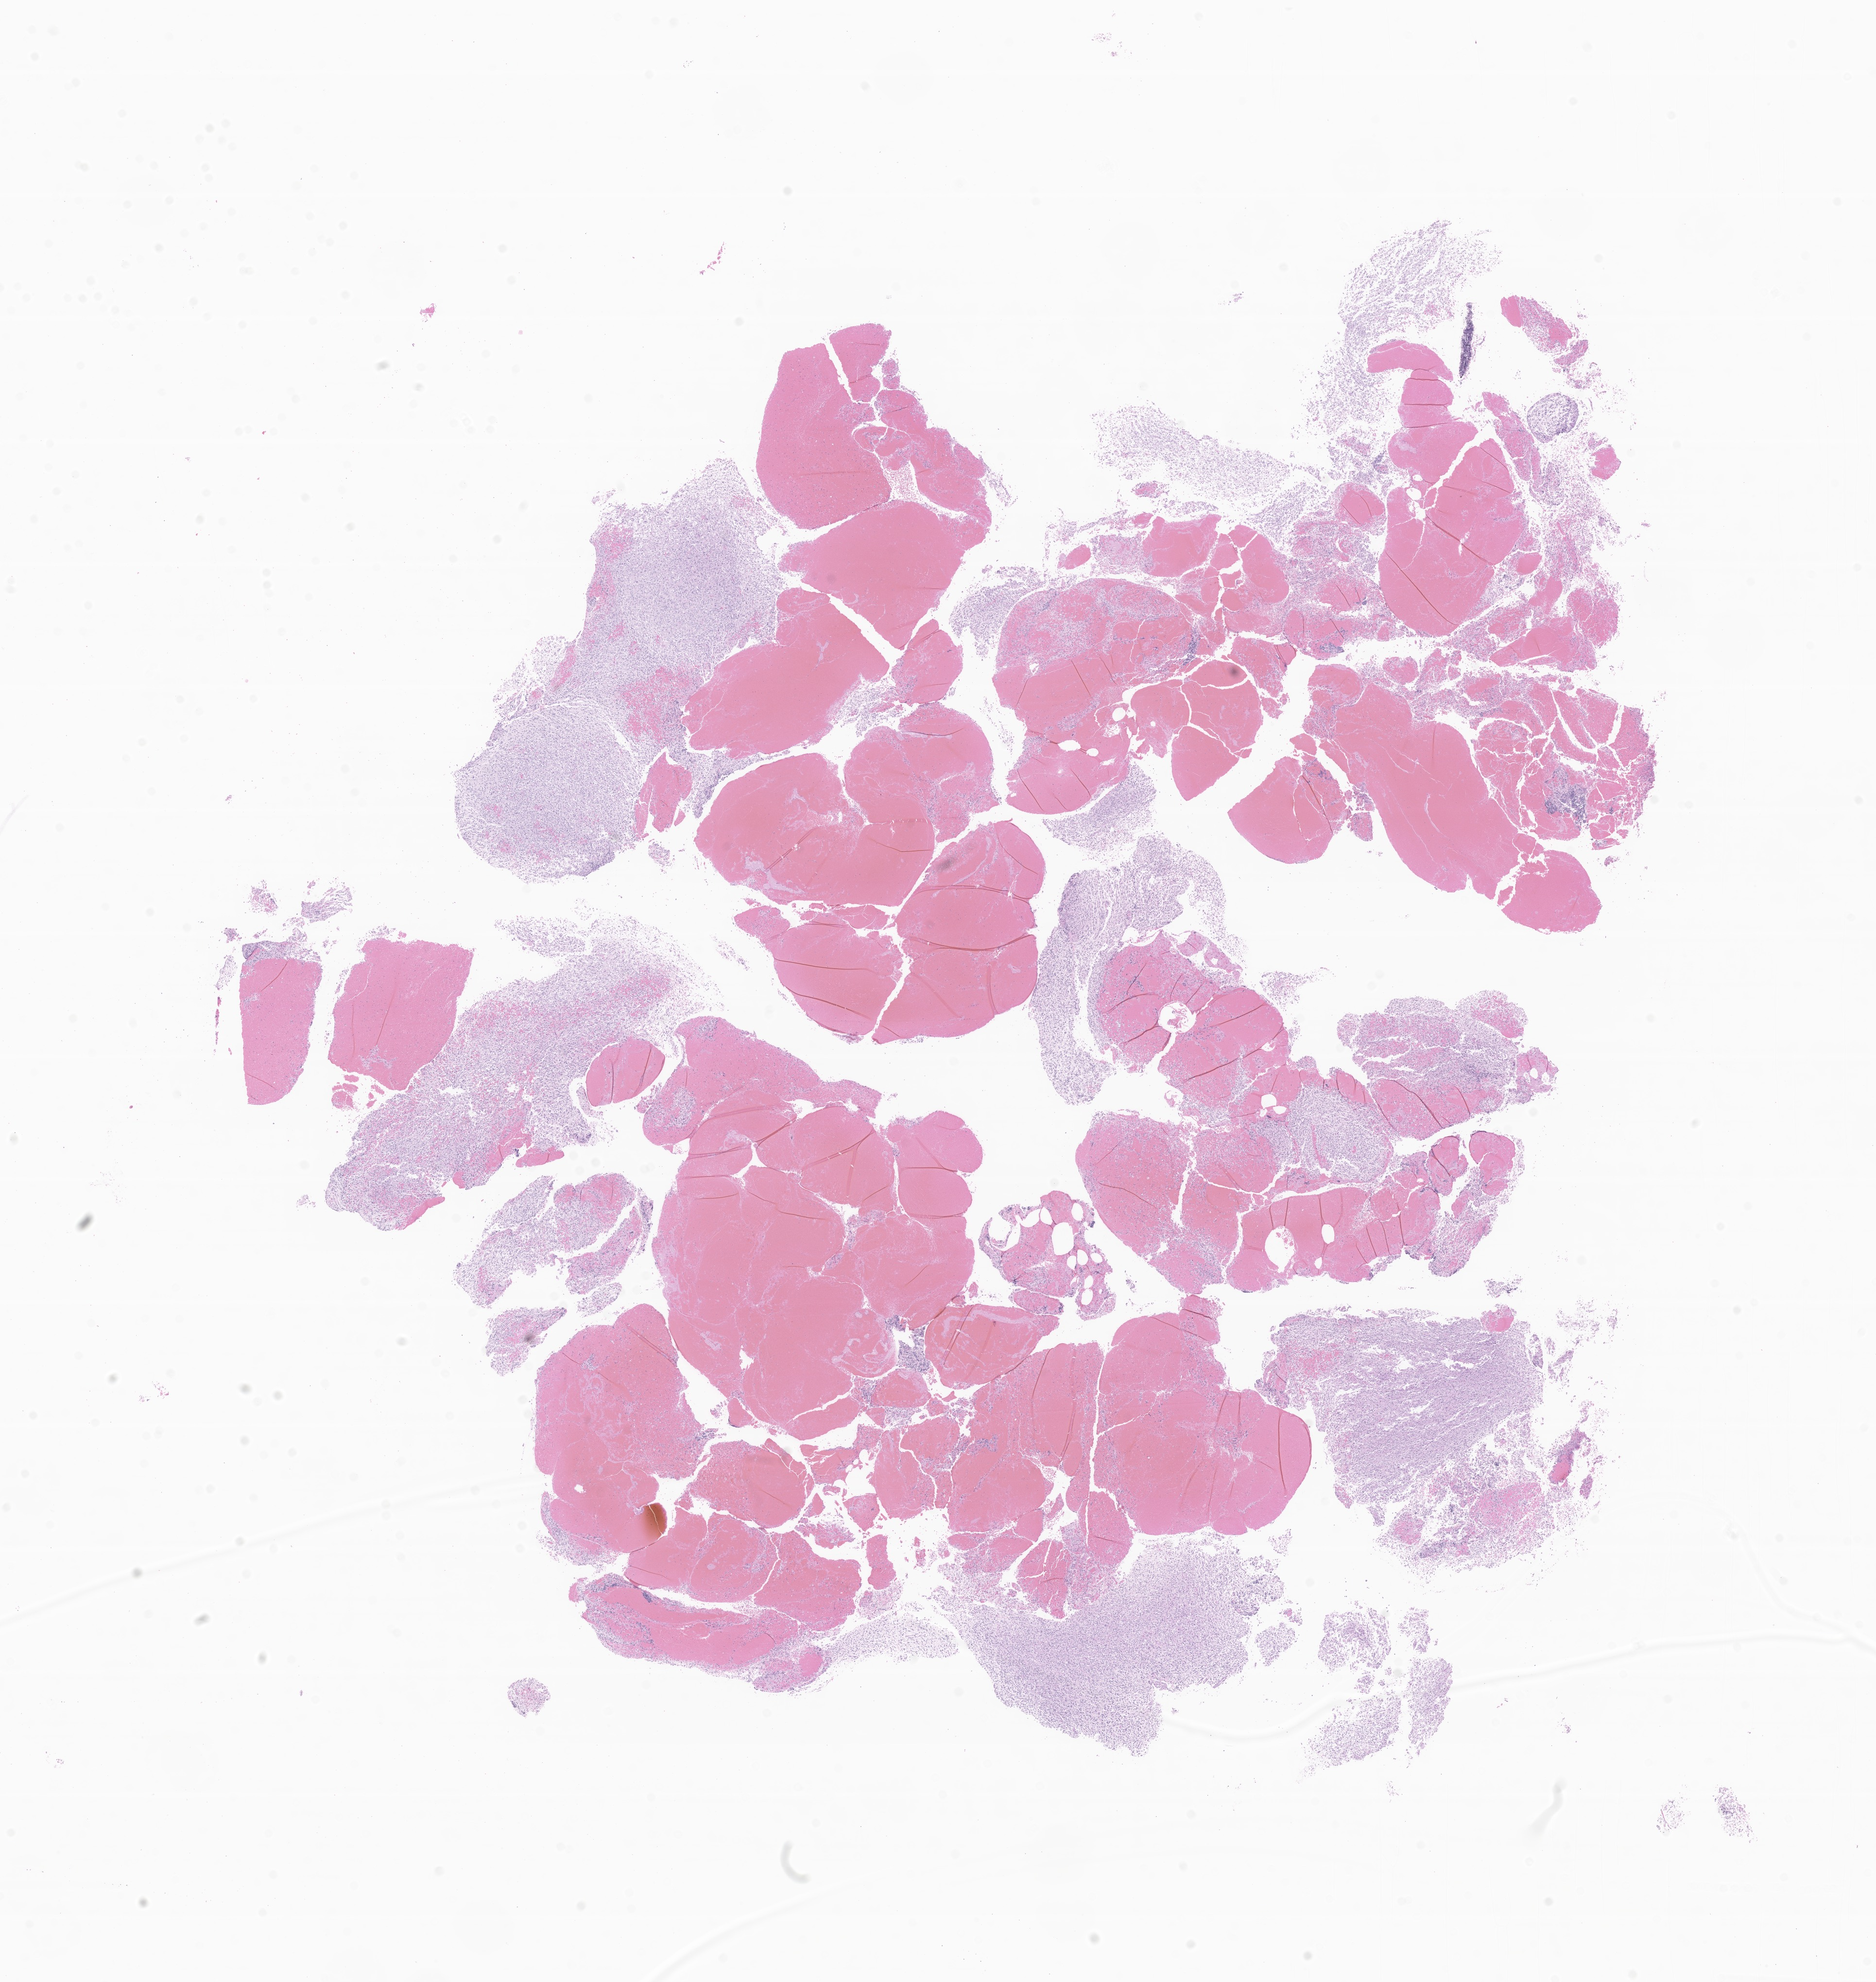
Digitized haematoxylin and eosin-stained section of tumor tissue from the brain — shown as a low-resolution overview of the whole scanned area (about 16.3 x 17.2 mm). Formalin-fixed paraffin-embedded section. Patient: male, age 200 months (16 years 8 months).
Recorded diagnosis: Neoplasm, malignant.